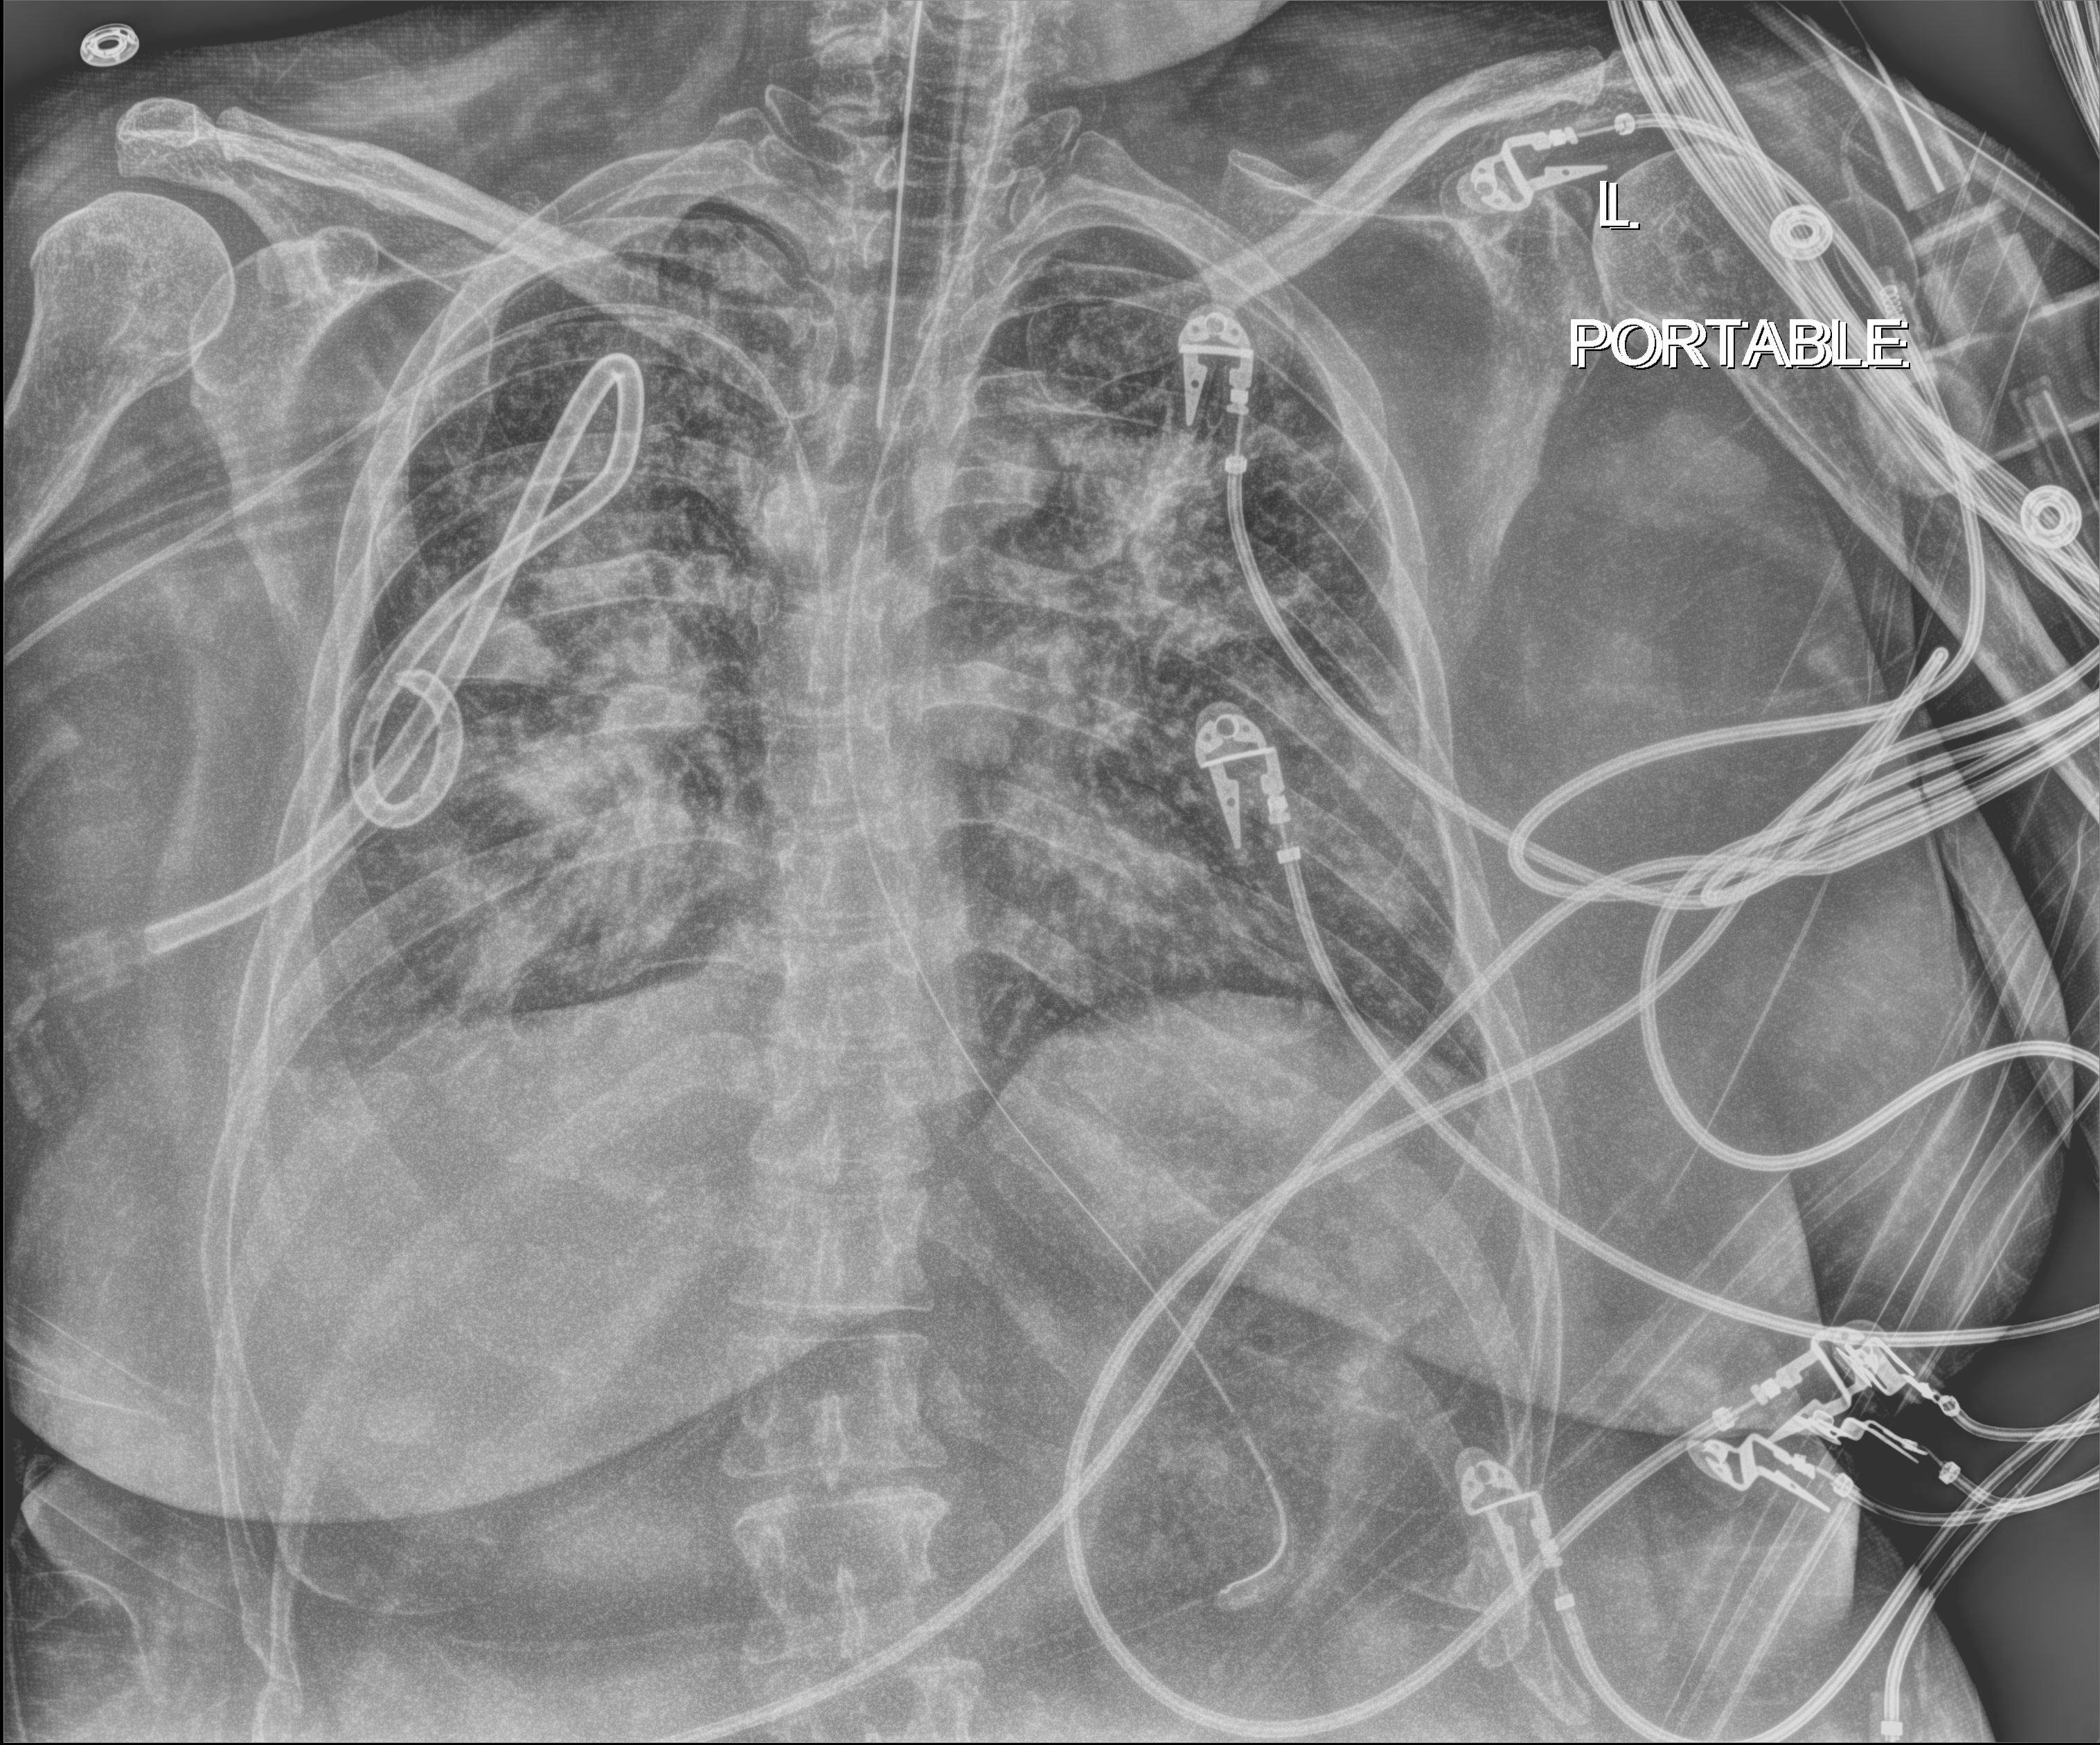
Bedside chest radiograph (digital radiography). Patient hospitalised with COVID-19, aged 18–59 years.
From the hospital-stay record, not from the radiograph (when in the stay this image was taken is not recorded): mechanically ventilated during this hospital stay: yes.